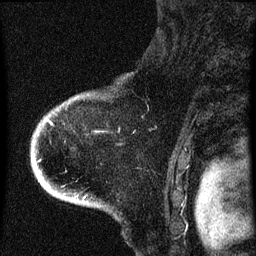
Breast MRI (dynamic contrast-enhanced), one sagittal slice; slice 53 of 60 in the series (ordered by position); dynamic contrast-enhanced series, image 2 of 4 at this slice position (ordered by acquisition); 1.5 T; TE 4.2 ms, TR 8 ms; 2 mm slice thickness; 256 × 256 image matrix, field of view 180 × 180 mm. Female patient, age 71 years.
Structures marked on this image (semi-automatic segmentation, software-assisted and operator-edited):
- analysis volume of interest (the breast-tissue region the enhancement analysis was run in; not a lesion): bounding box <32,90,119,205> (left, top, right, bottom; pixels)
- tumour enhancement mask (voxels above the 70 % enhancement threshold inside the analysis volume of interest): <38,122,52,161>